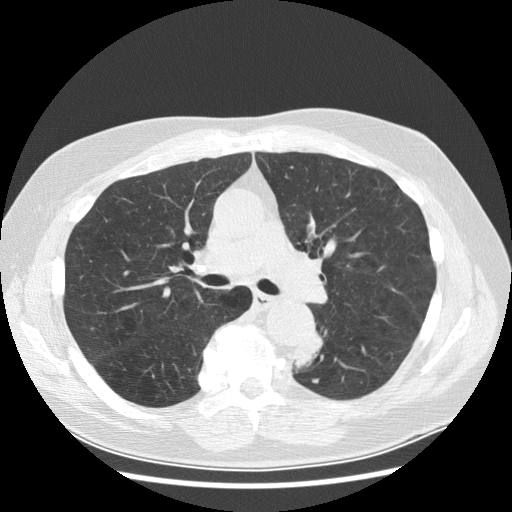
Low-dose screening chest CT, one axial slice. Slice 176 of 282 in the series (ordered by position). Reconstruction kernel STANDARD. Lung window (W 1500 / L -600 HU). 512 × 512 image matrix.
Outlined on this slice (manually delineated by an expert):
- lesion 1 (tumor, lower lobe of left lung): bounding box (x1, y1, x2, y2) in pixels: (293, 331, 323, 369)